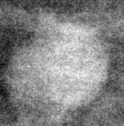
Region of interest cut from a scanned film mammogram (one marked finding); right breast; MLO view; BI-RADS breast density category 1 (scale 1–4).
- Finding: mass, shape lymph node, margins circumscribed; BI-RADS assessment category 2; benign; no additional work-up was recommended (benign without callback).